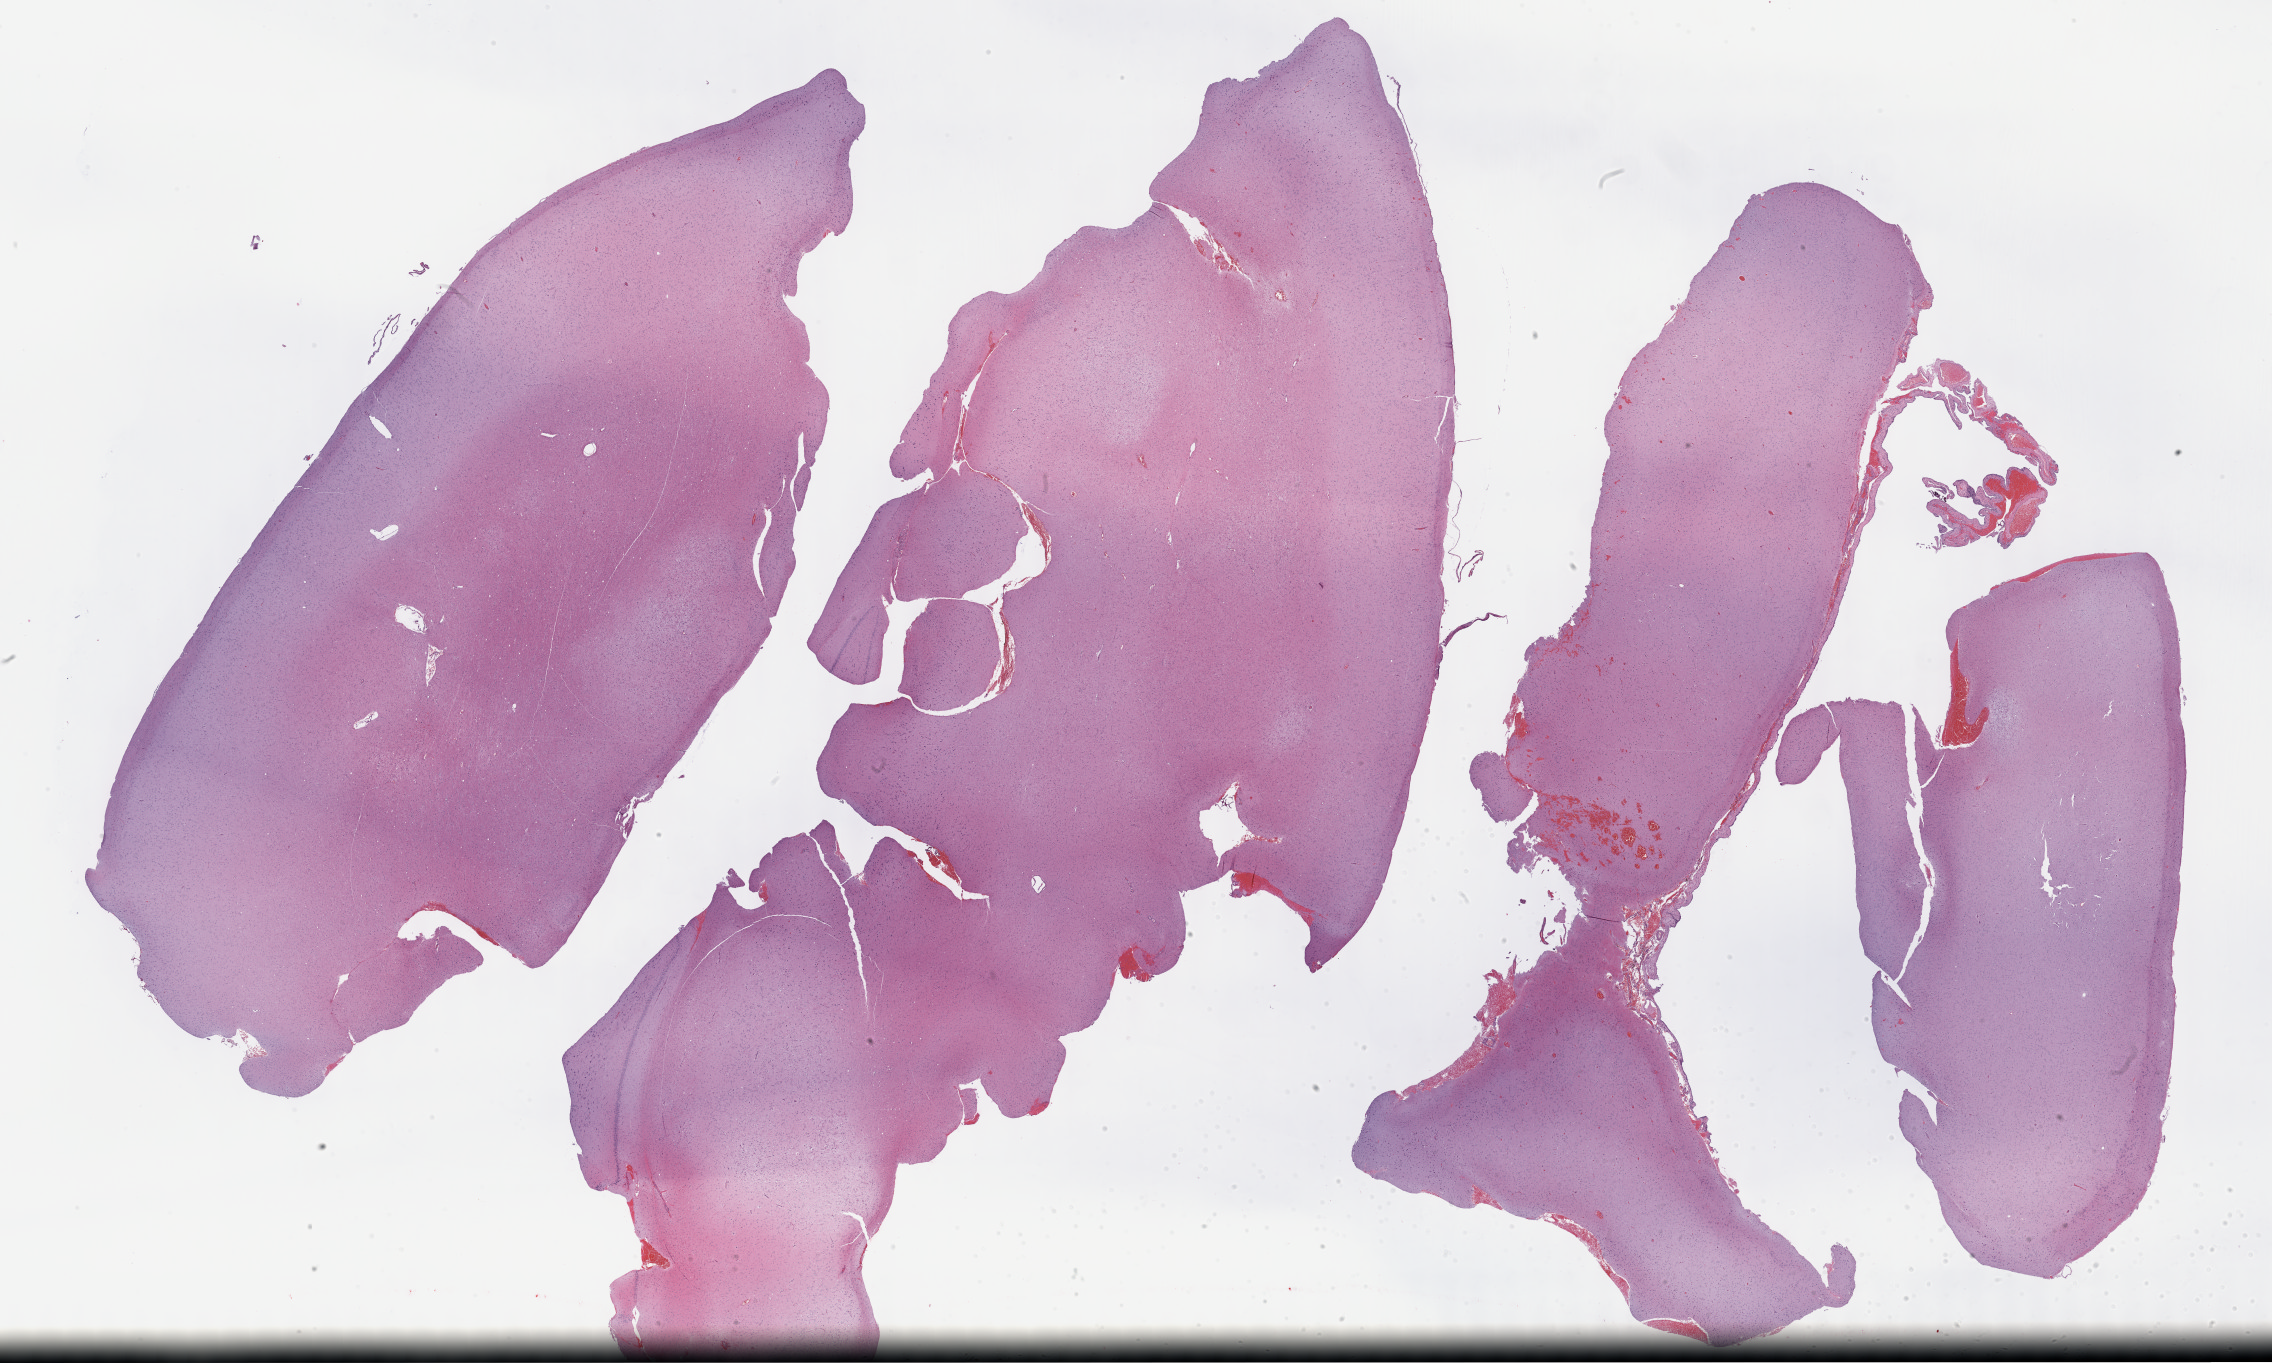
Digitized H&E-stained tissue section (whole slide), shown as a low-resolution overview of the whole scanned area (about 36.7 x 22.0 mm, acquisition: 40x scan), formalin-fixed paraffin-embedded (FFPE) diagnostic section, brain, primary tumour sample. Female, age 37 years at initial diagnosis. Histologic grade: G2 (moderately differentiated).
- diagnosis: Astrocytoma, NOS (cerebrum)